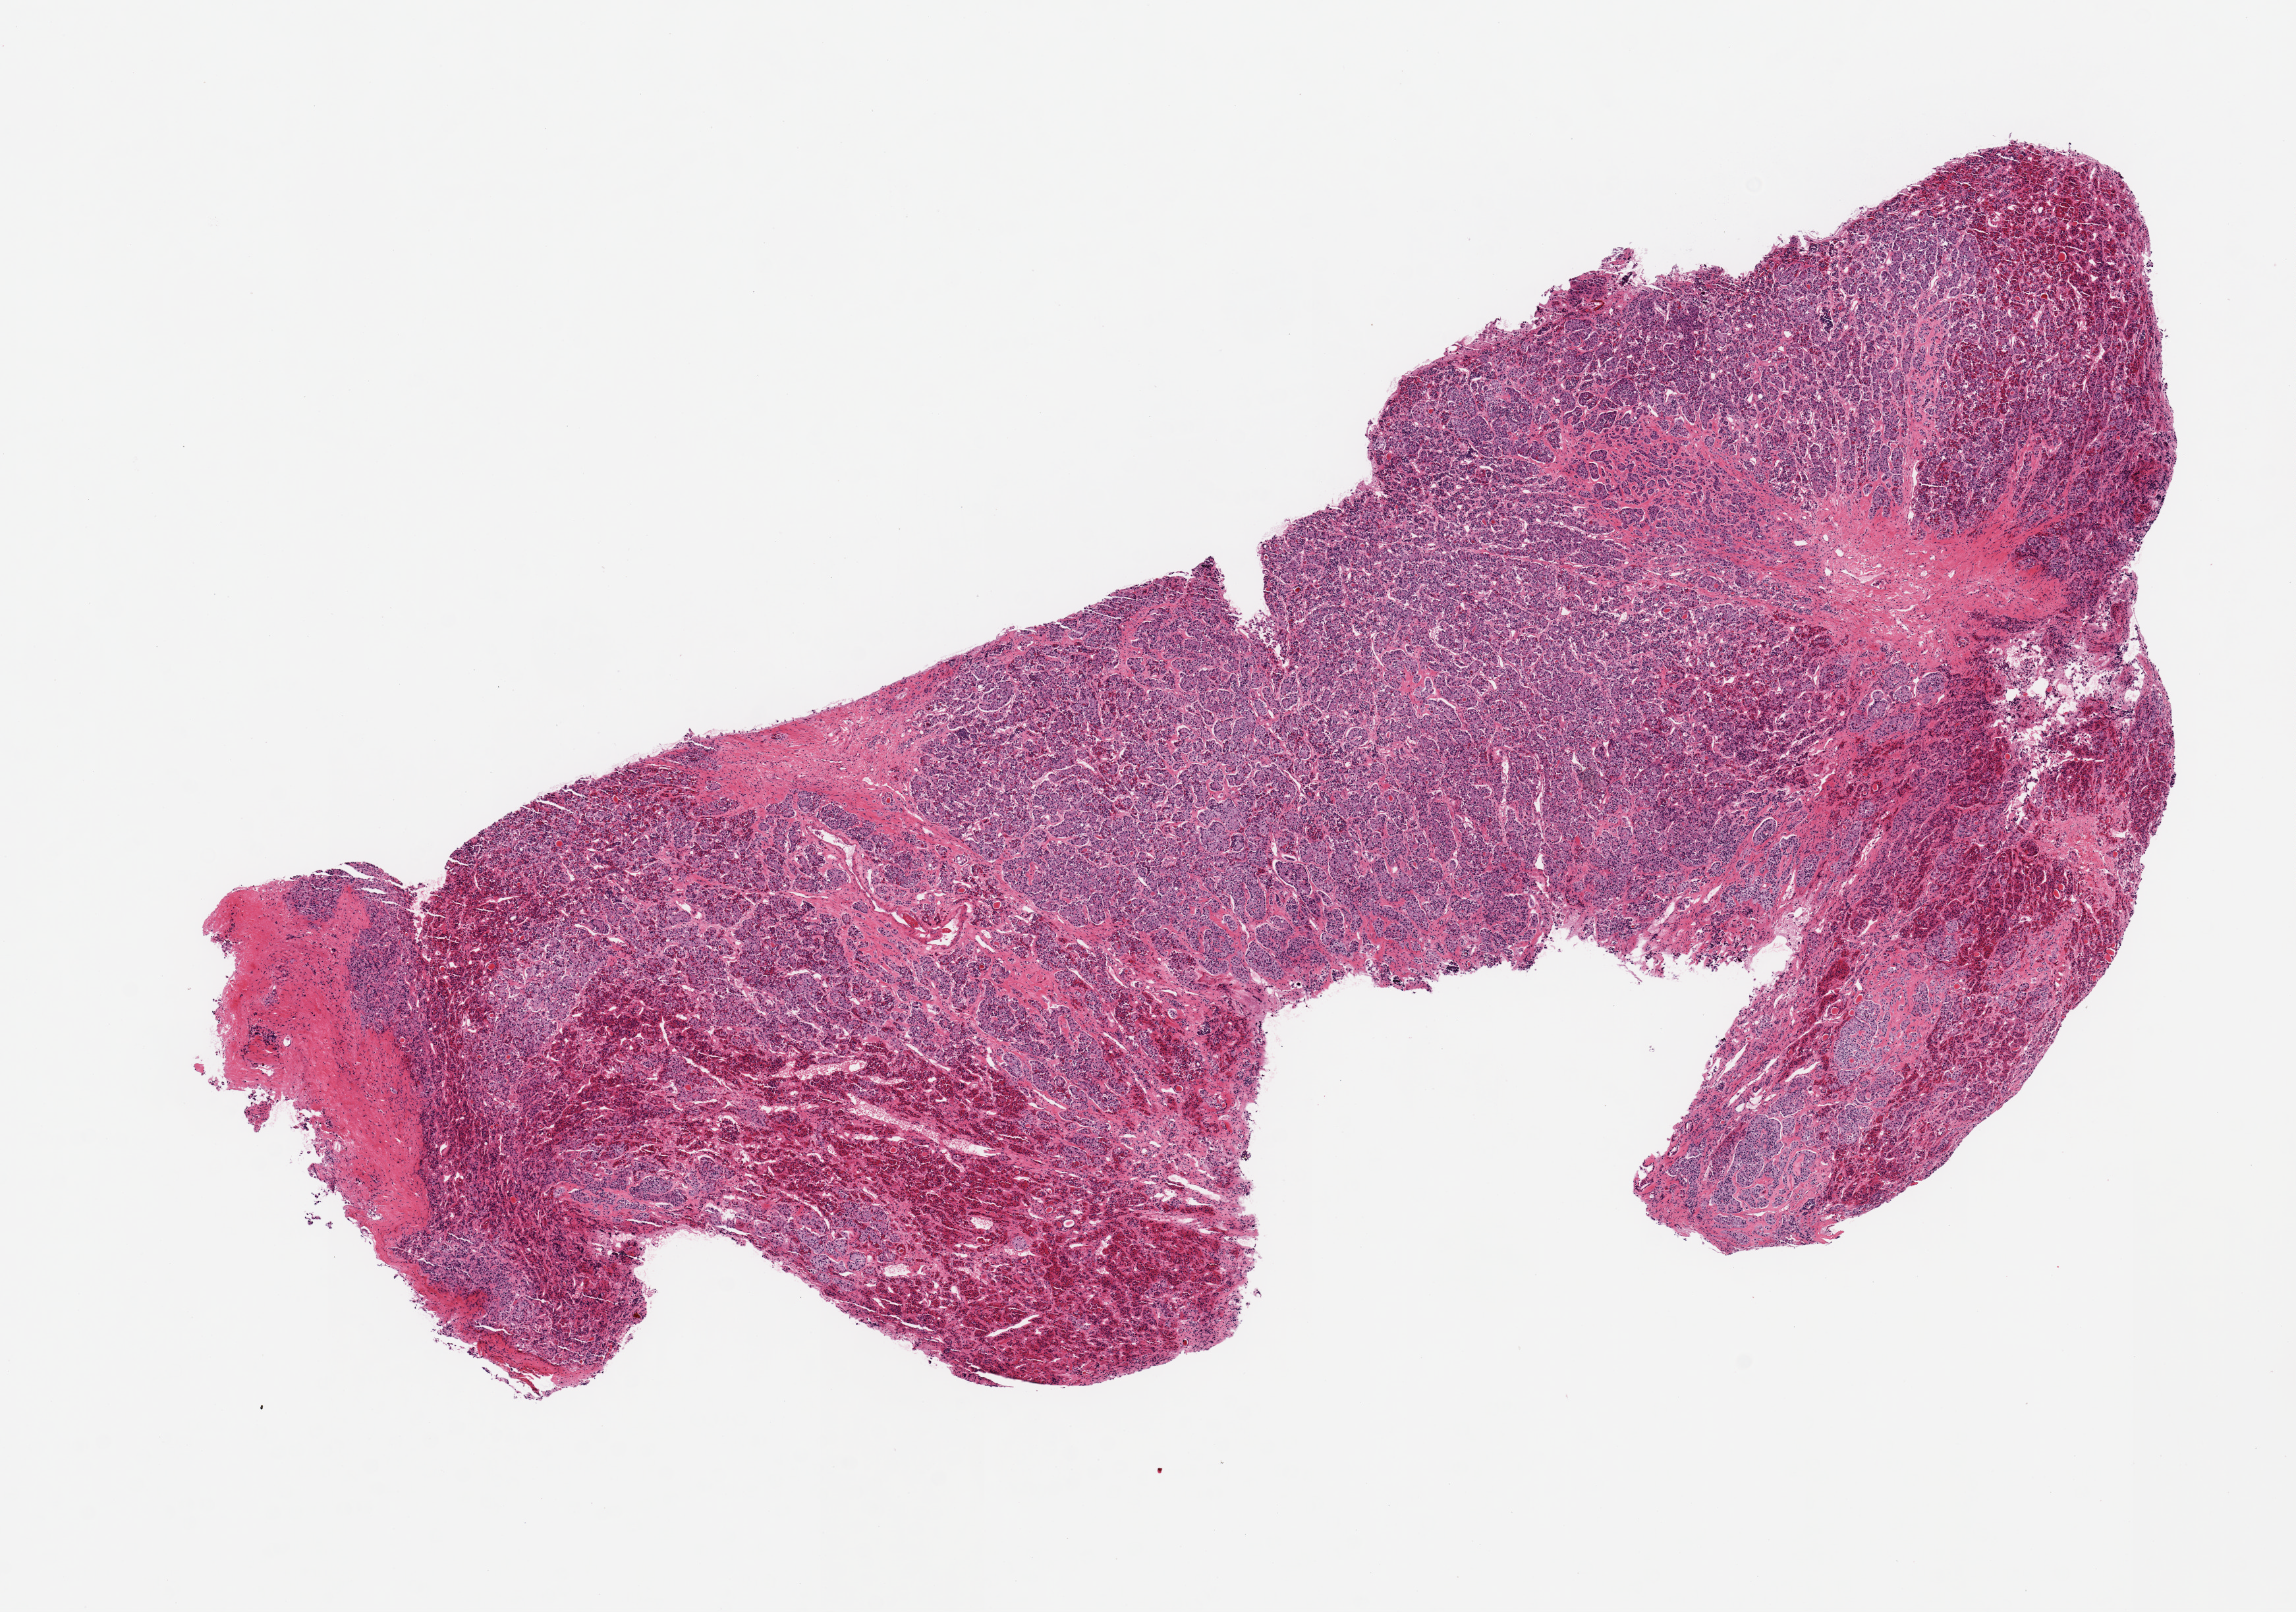
Digitized hematoxylin and eosin (H&E)-stained section, a low-resolution overview of the entire scanned area, about 13.8 x 9.7 mm (acquisition: 20x scan). PAXgene-fixed, paraffin-embedded tissue. Sampled site (target tissue): pituitary. Tissue donor sample. Male donor.
Pathologist's review note for this sample: 1 piece, adenohypophysis.